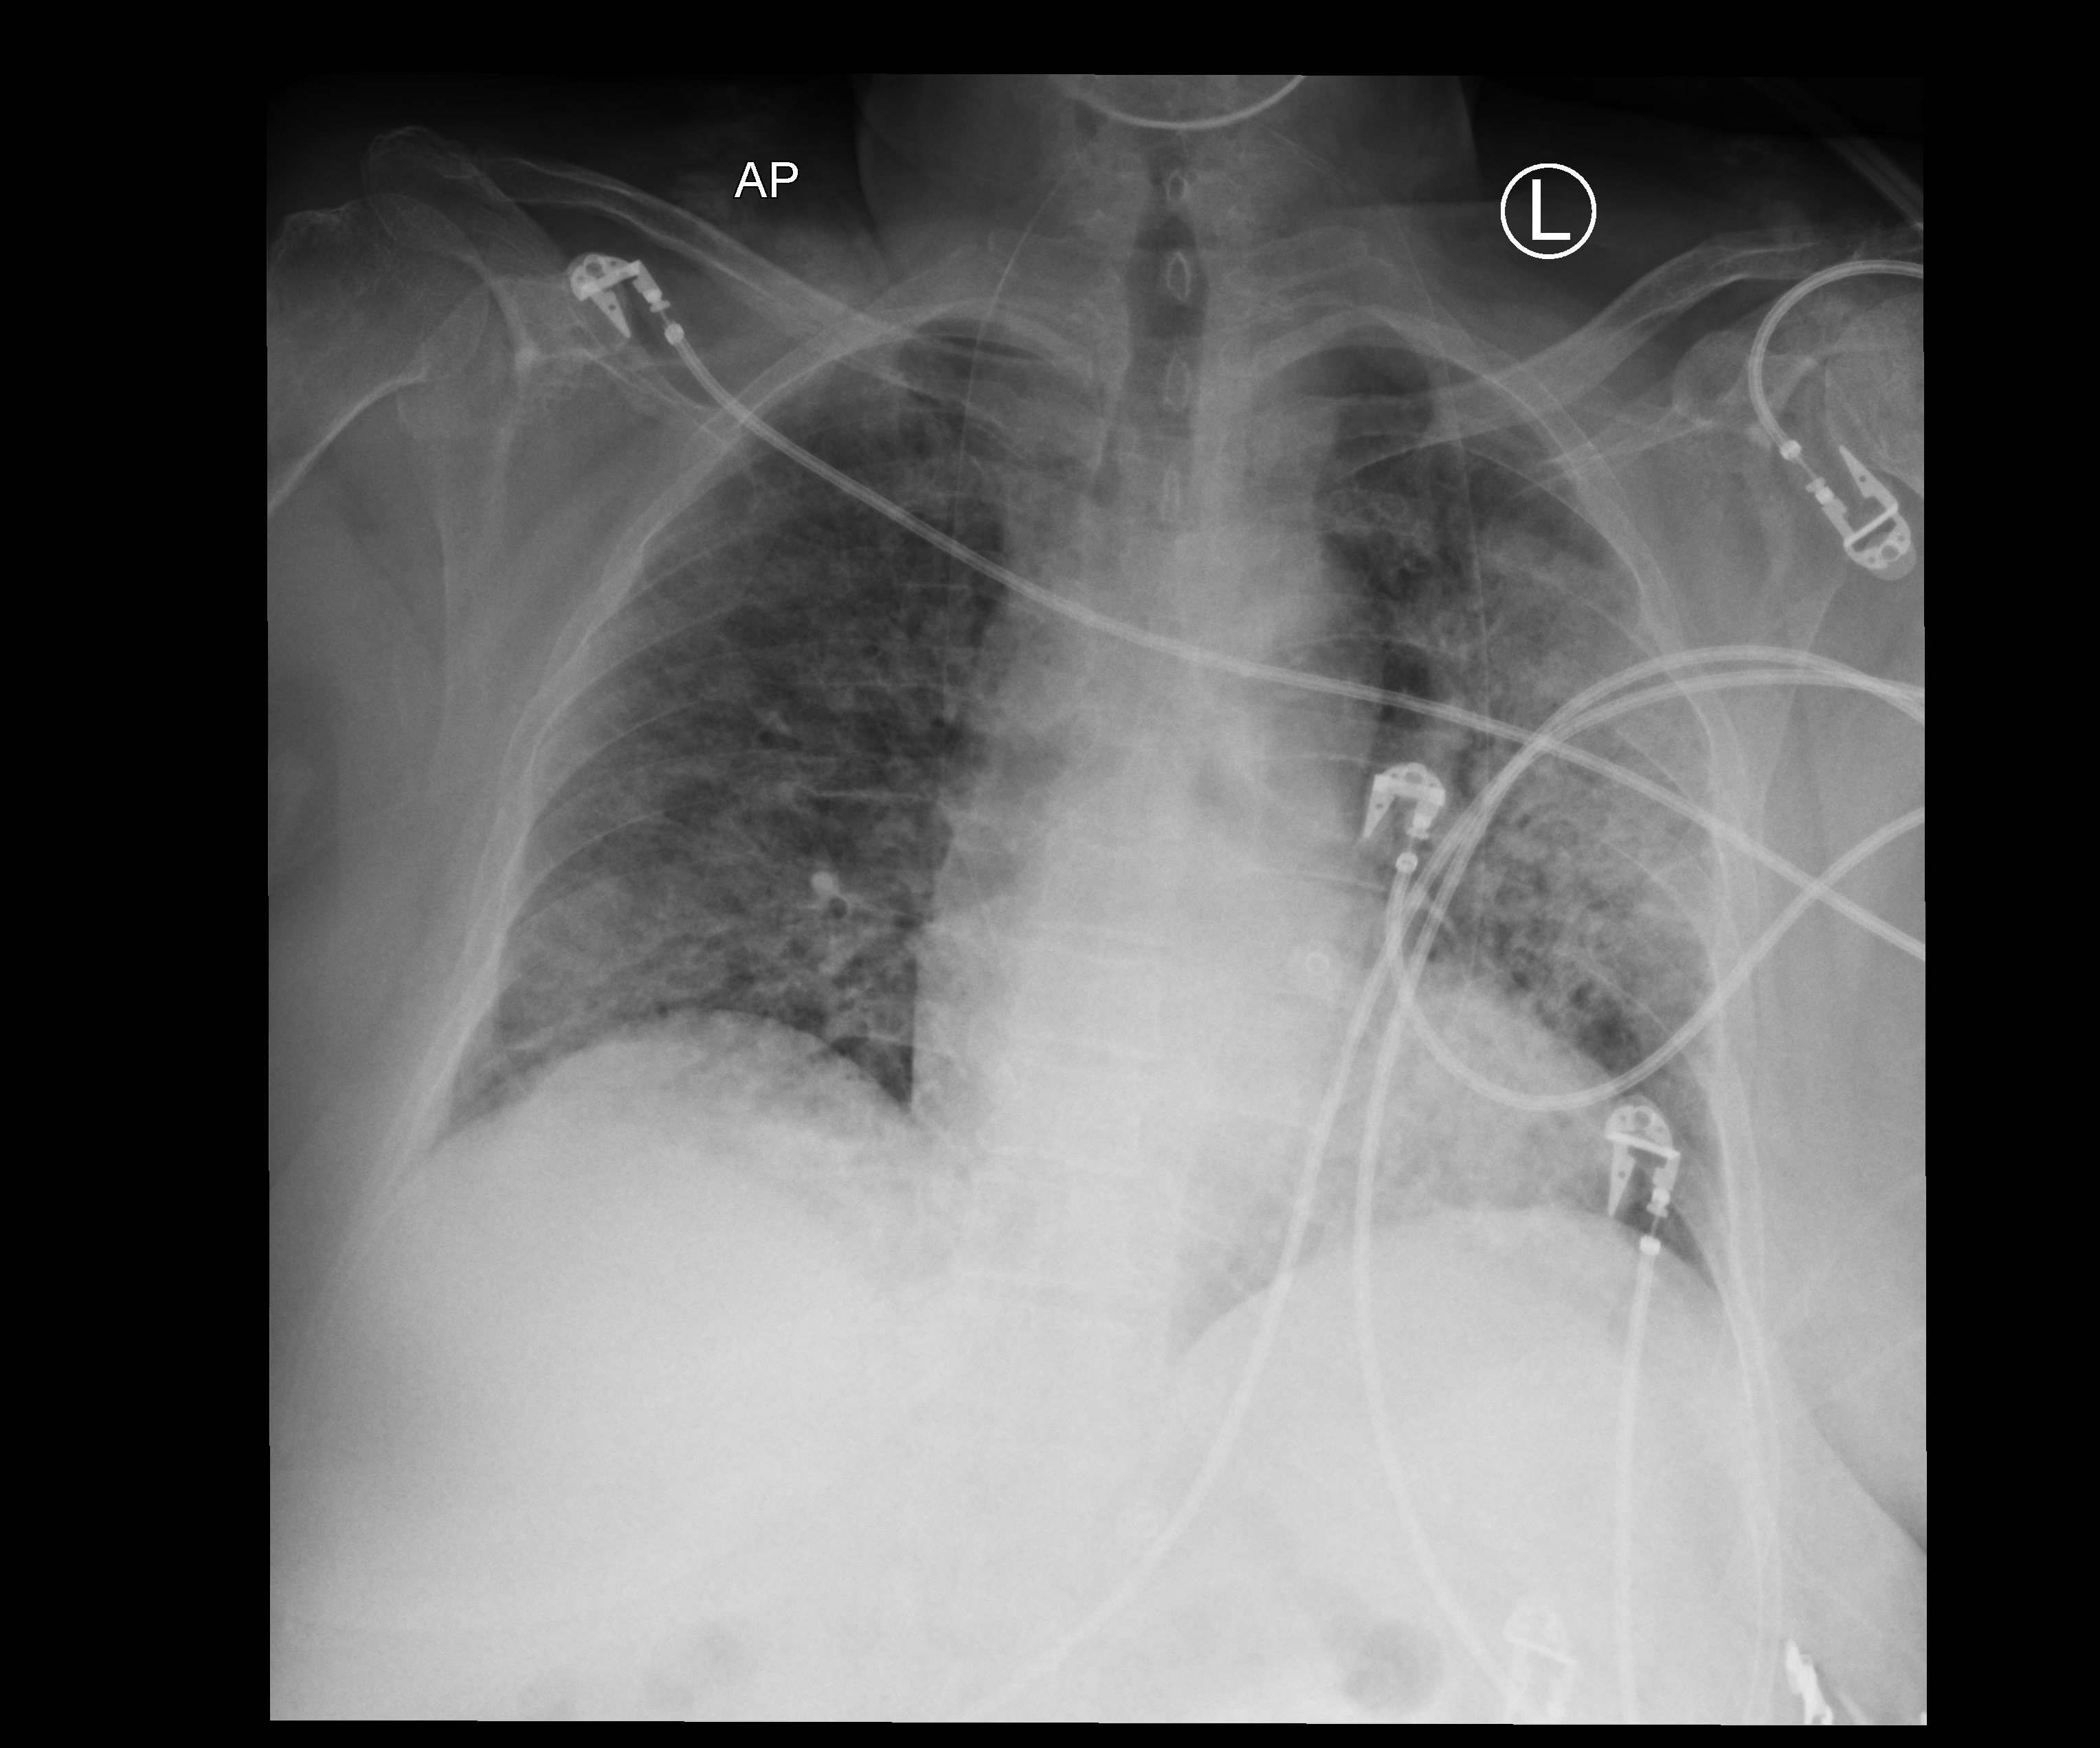
Chest X-ray (portable), anteroposterior (AP) projection. Female patient hospitalised with COVID-19, age 60–74 years.
From the hospital-stay record, not from the radiograph (when in the stay this image was taken is not recorded):
- admitted to intensive care during this hospital stay: yes
- mechanically ventilated during this hospital stay: no